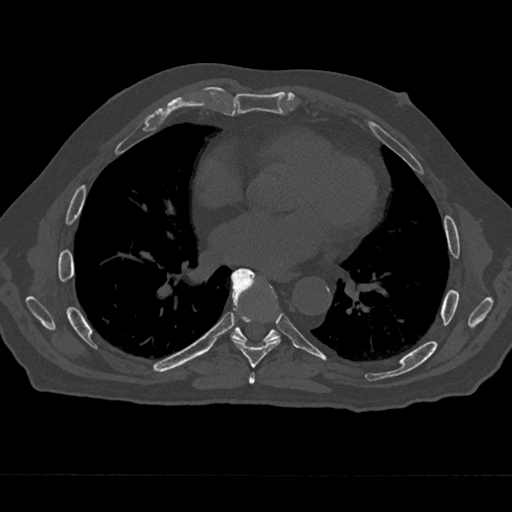
CT including the spine, one axial slice. Slice 349 of 797 in the series (ordered by position). Reconstruction kernel Br40s/3. 120 kVp. Bone window (W 1800 / L 400 HU). 0.5 mm slice thickness. 512 × 512 image matrix, field of view 377 × 377 mm. Male patient, age 75 years. From the clinical record (not read from this slice): primary cancer: renal.
Outlined on this slice (semi-automatically segmented with operator editing):
- T6 vertebra: bounding box [x1, y1, x2, y2] px = [249, 372, 255, 384]
- T7 vertebra: [232, 268, 281, 368]
- T8 vertebra: [230, 272, 280, 343]